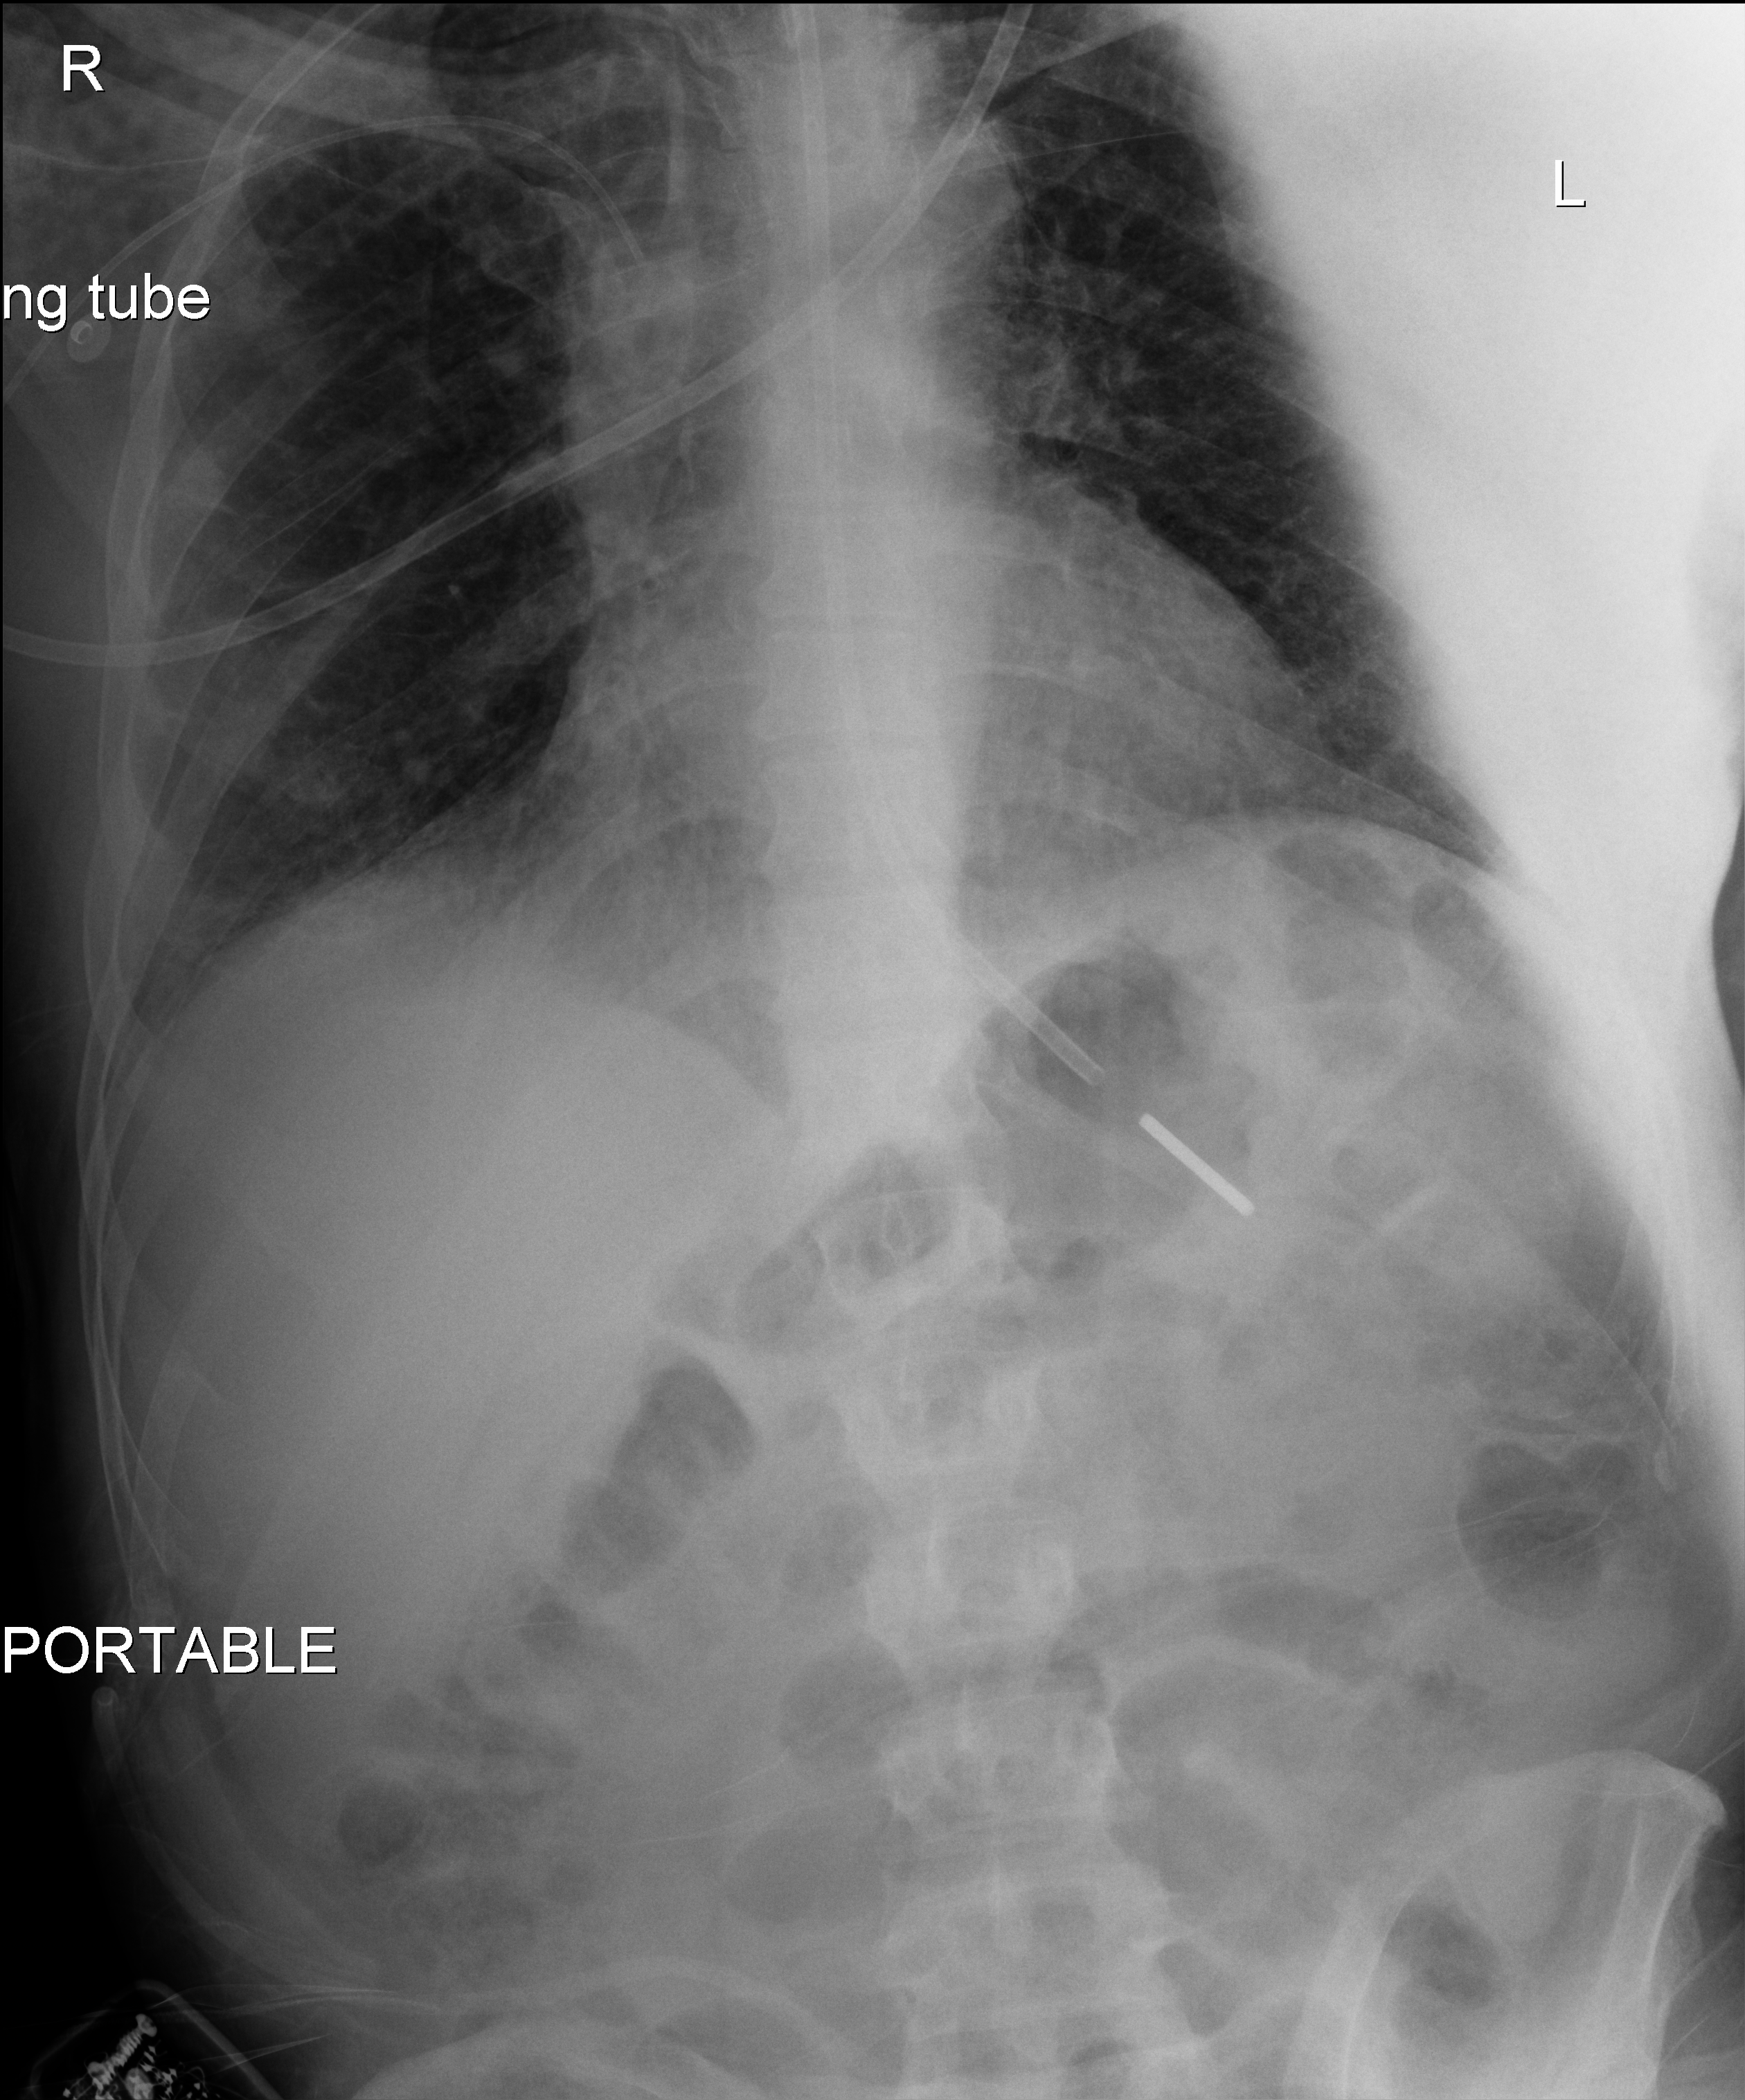
Portable chest radiograph, anteroposterior (AP) projection. Male patient hospitalised with COVID-19, age 18–59 years.
Hospital-stay facts (about this admission, not read from this image; timing relative to this image not recorded):
- smoking status (admission record): never